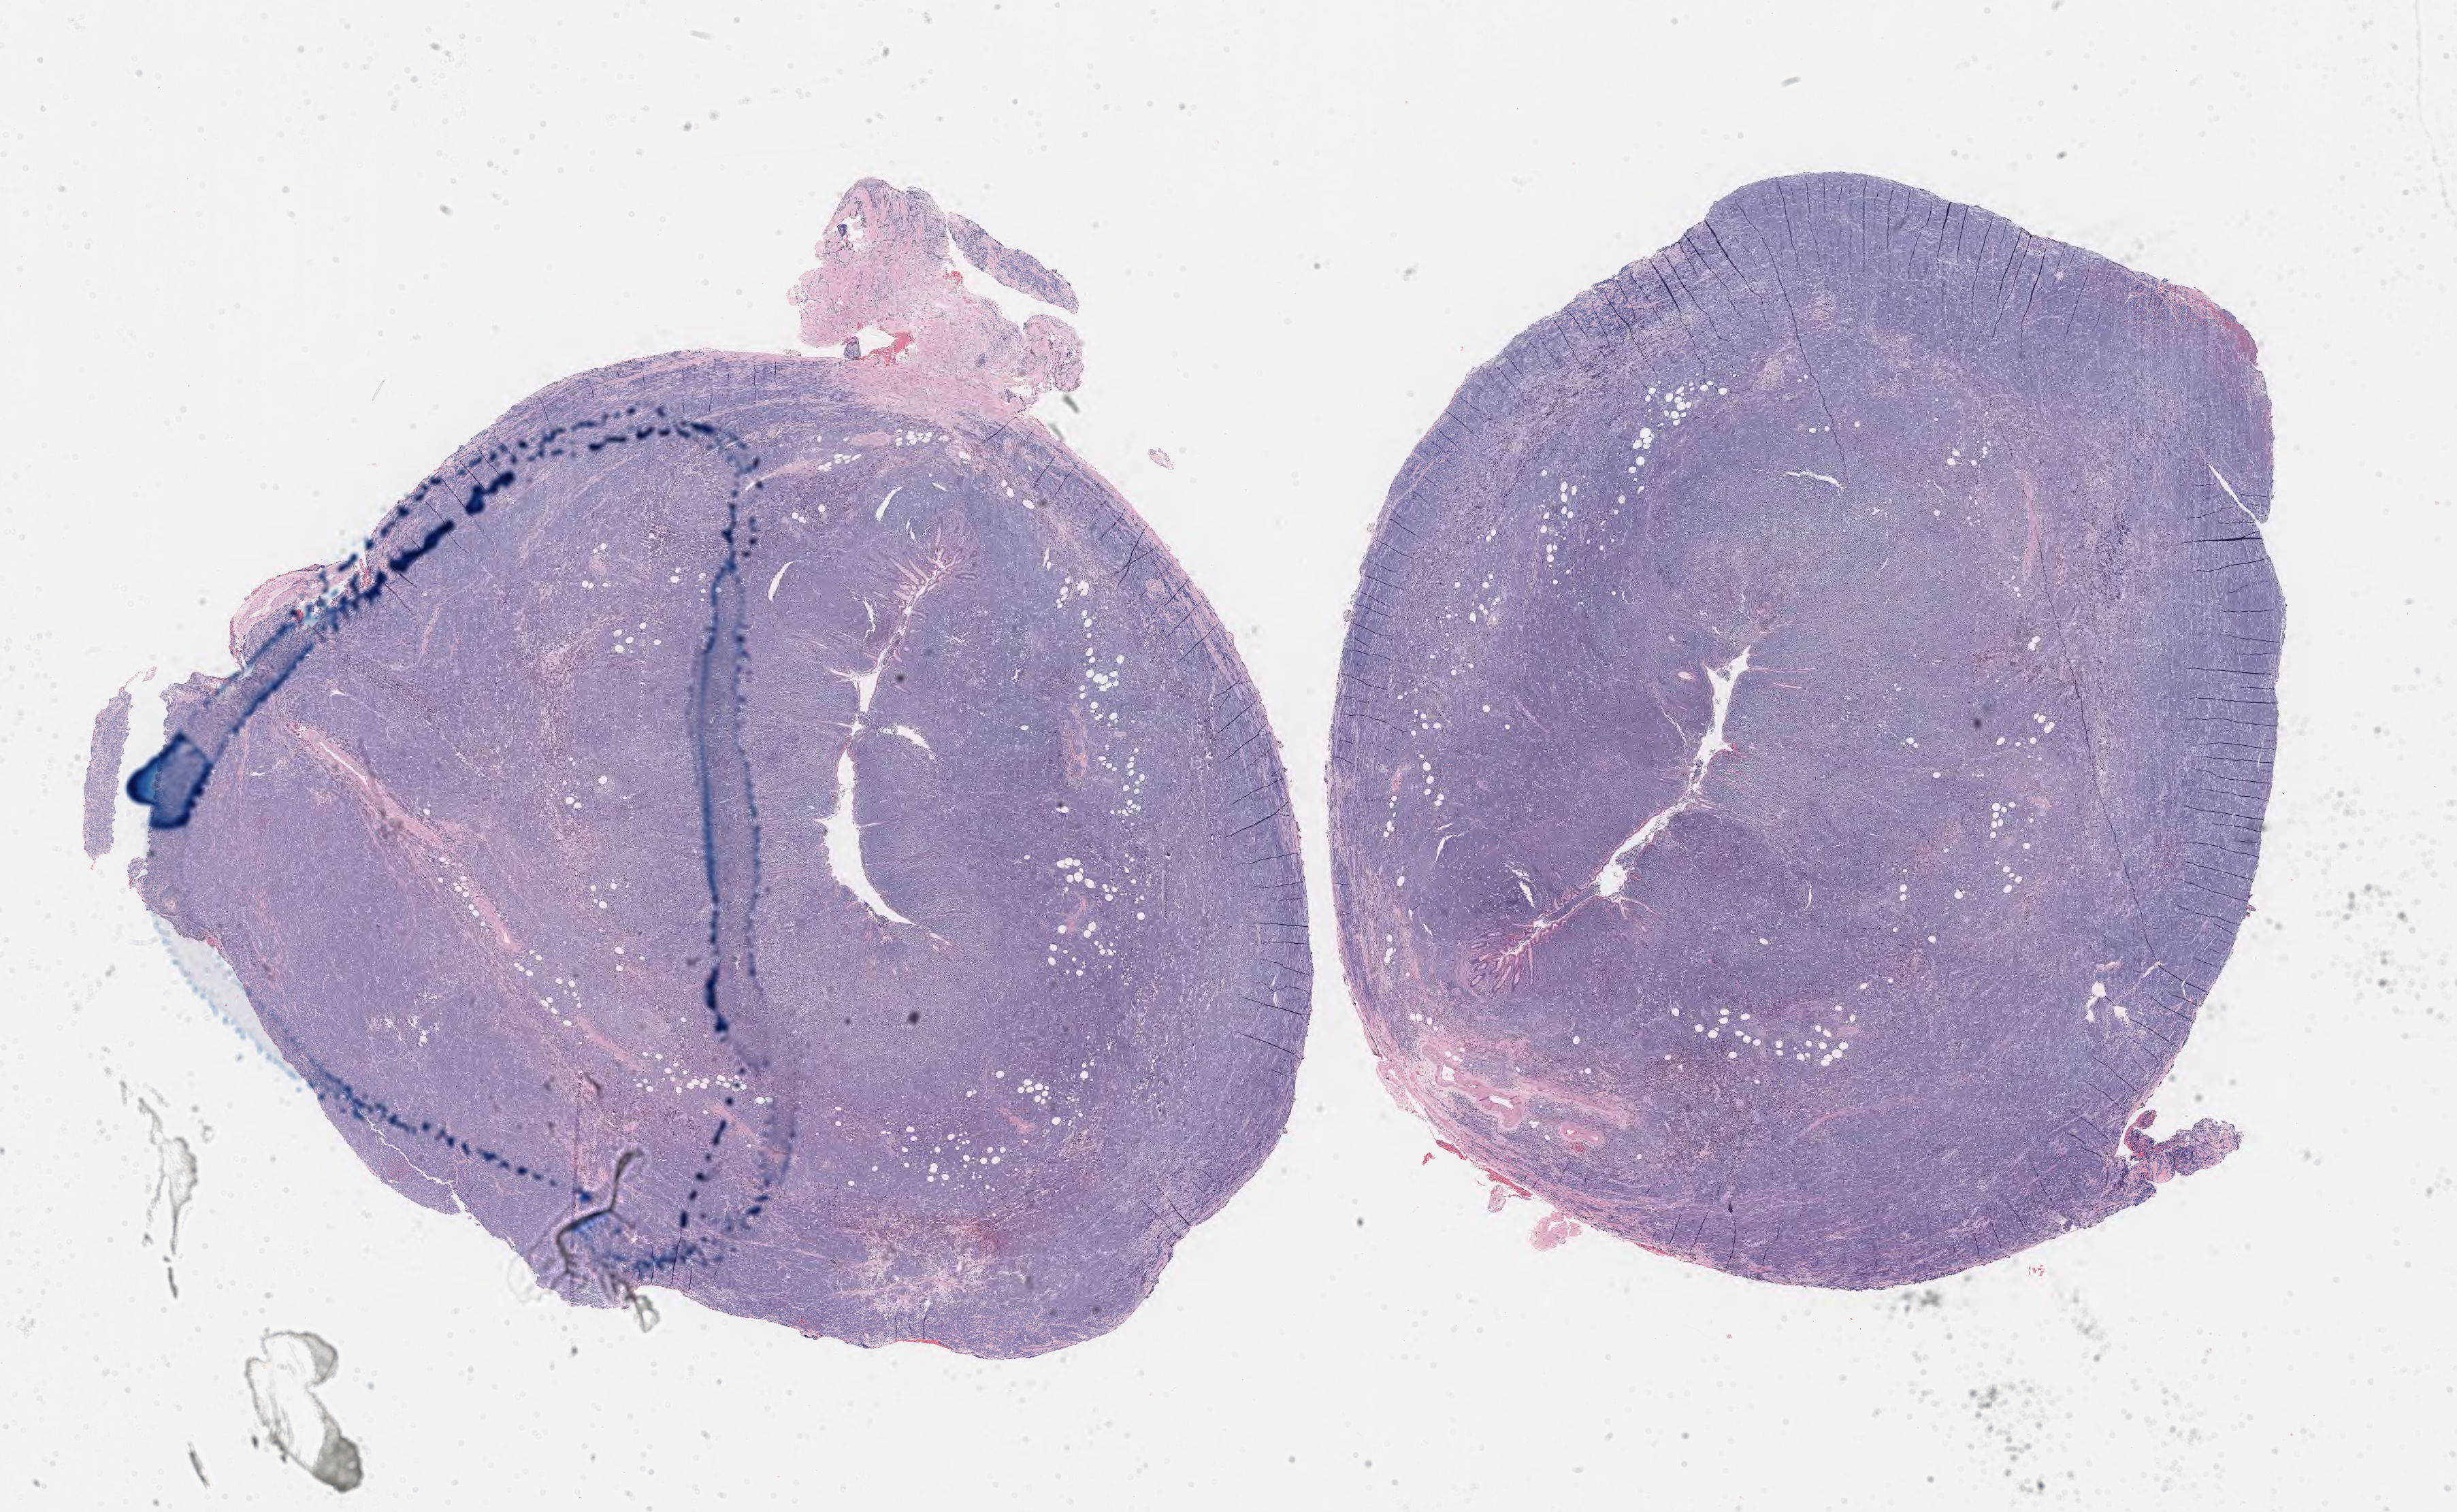
Whole-slide image, haematoxylin and eosin stain, shown as a low-resolution overview of the whole scanned area (about 29.2 x 18.0 mm). Specimen: tumor tissue. Patient male; aged 63.
* diagnosis: Diffuse large B-cell lymphoma, NOS